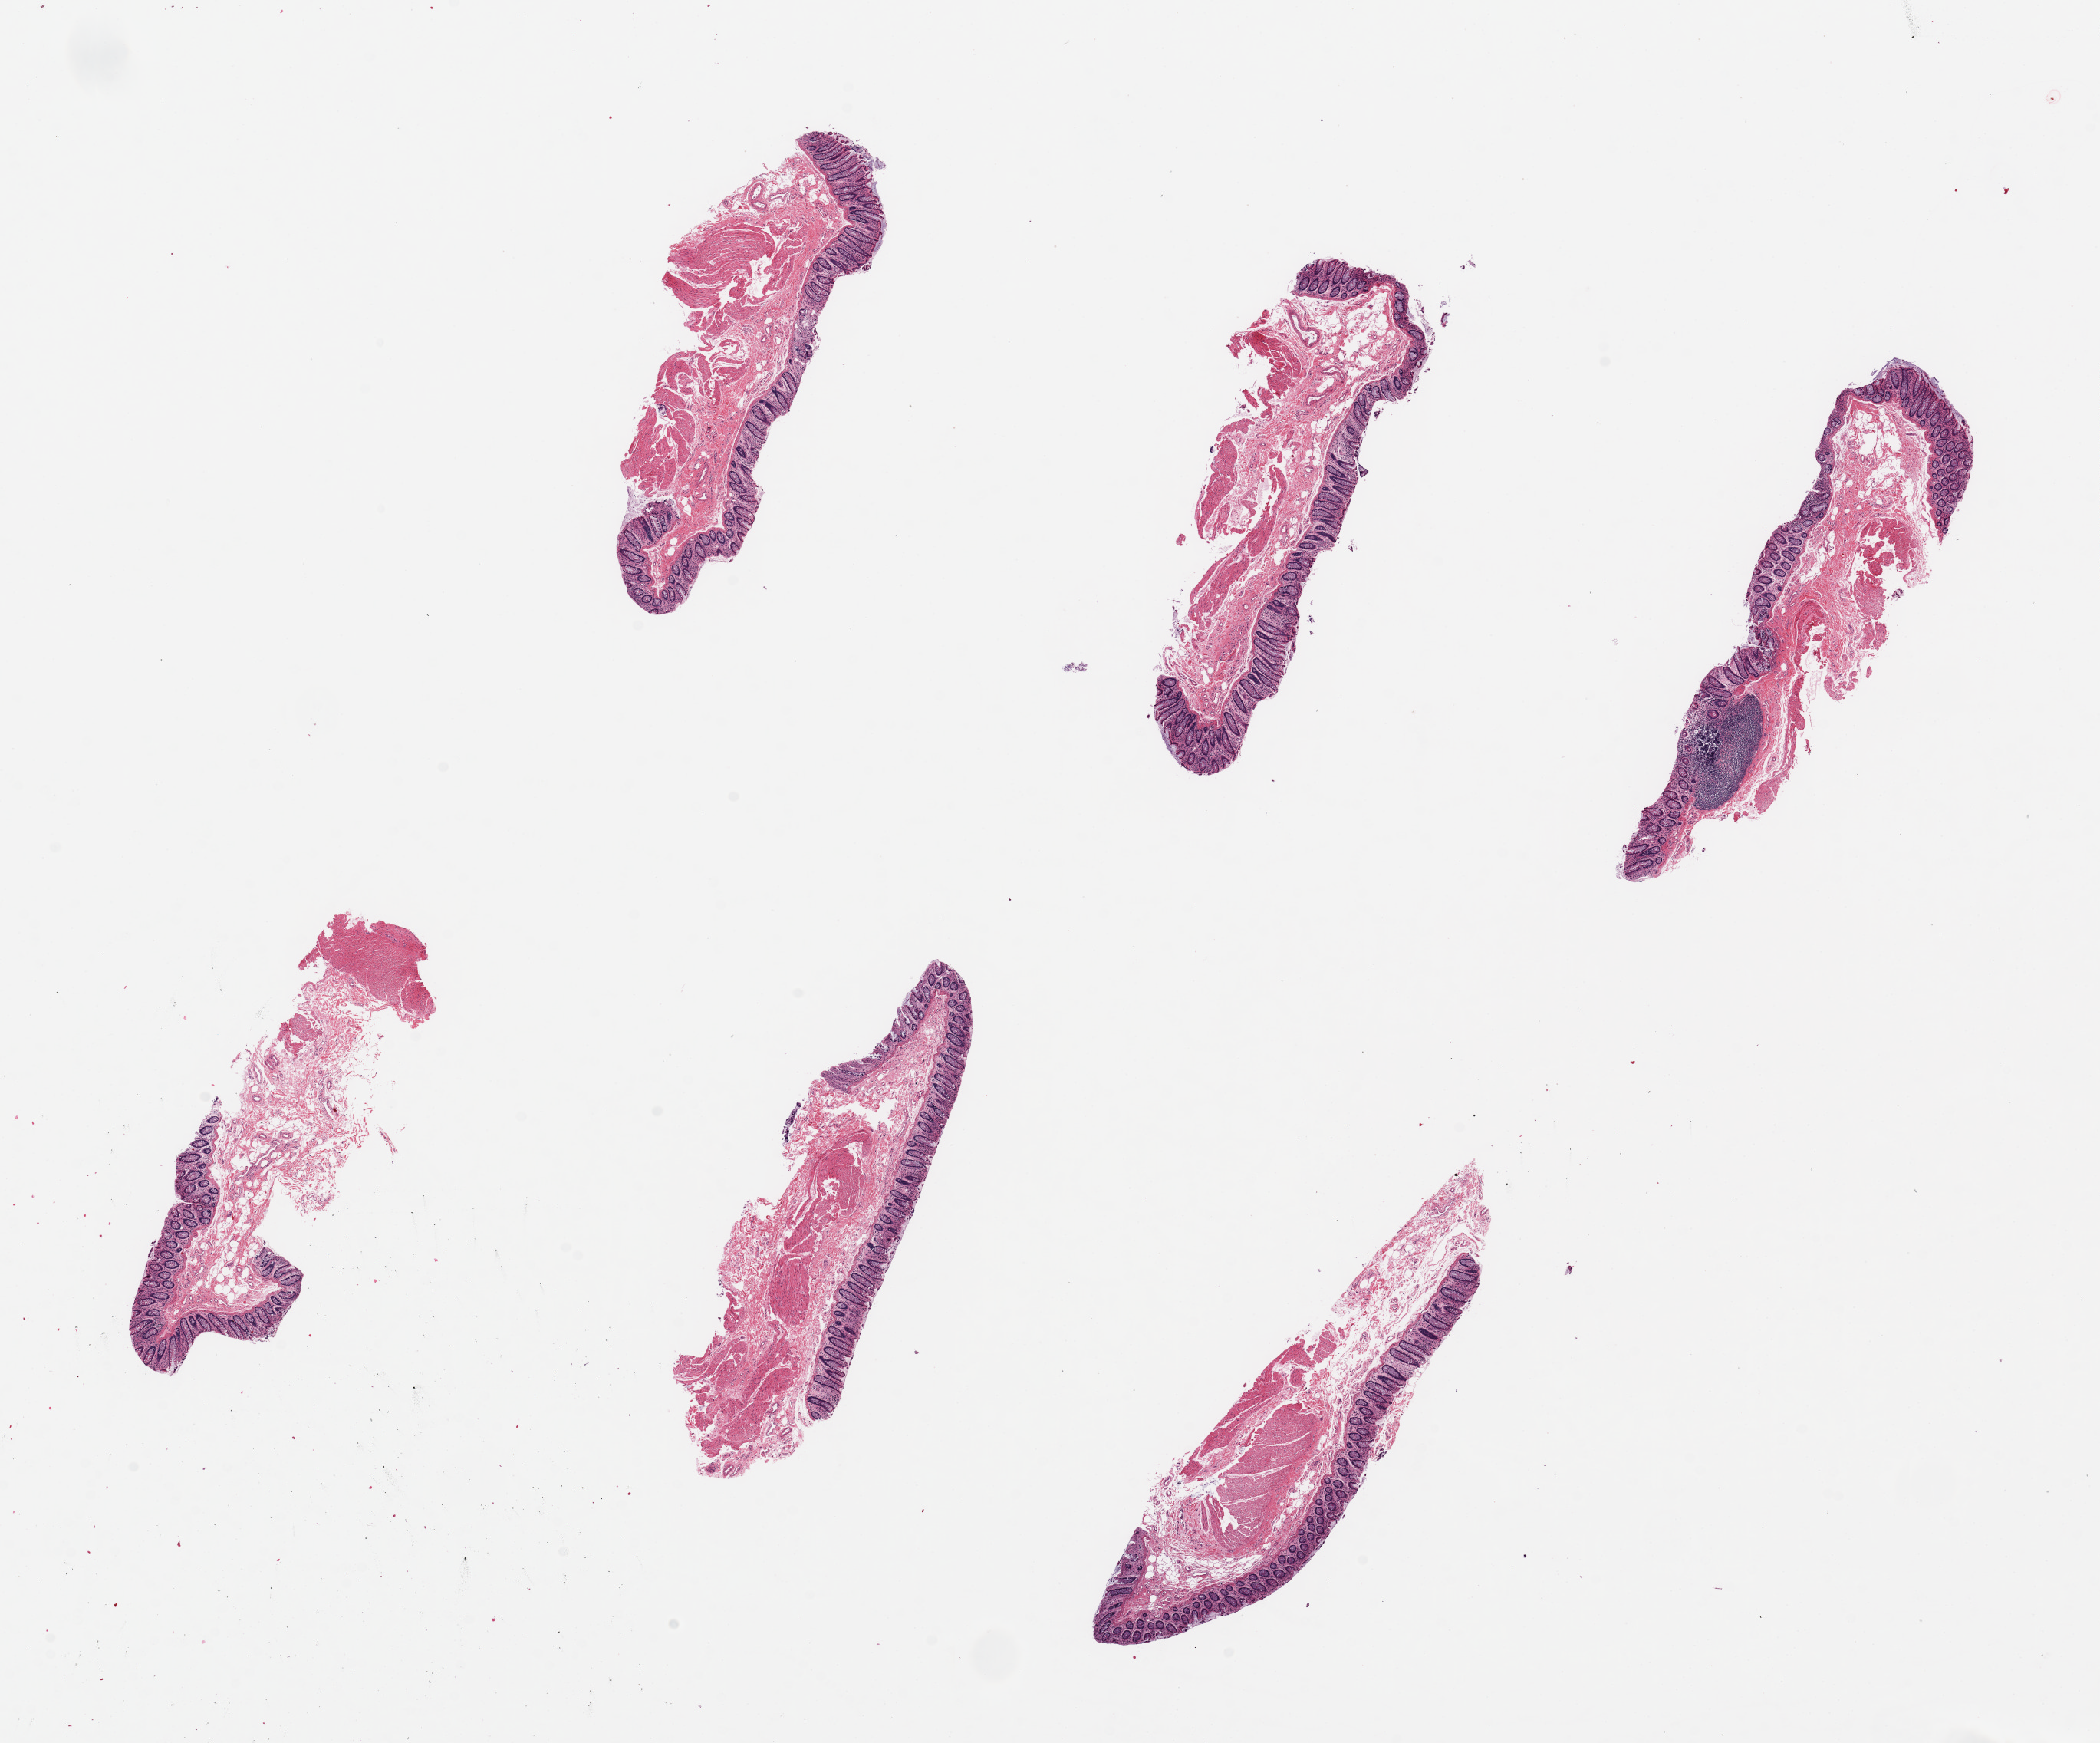
Digitized hematoxylin and eosin (H&E)-stained section, brightfield — shown as a low-resolution overview of the whole scanned area (about 21.7 x 18.0 mm), PAXgene-fixed paraffin-embedded (PFPE) section, section of transverse colon (target tissue), donor tissue sample. Donor: male.
Reviewer comment on this tissue sample: 6 pieces ~6x1.5mm ?sigmoid? mucosa is 20% of thickness, trace muscle.